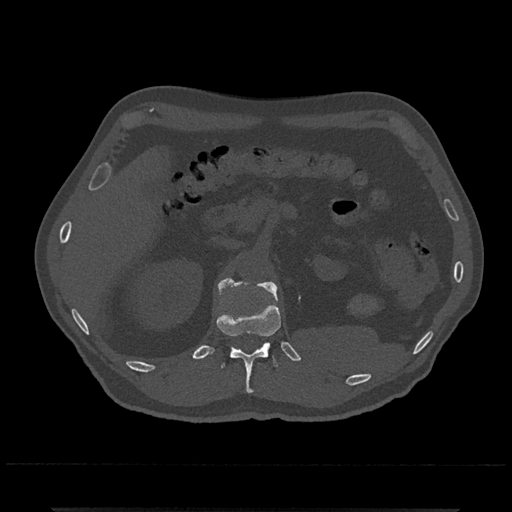
CT including the spine, one axial slice; slice 414 of 797 in the series (ordered by position); reconstruction kernel Br40s/3; 120 kVp; bone window (W 1800 / L 400 HU); 512 × 512 image matrix, field of view 393 × 393 mm. Patient: male, 67 years. Case-level facts recorded for this patient, not image findings: primary cancer: prostate.
Structures marked on this image (semi-automatic segmentation, software-assisted and operator-edited):
- L1 vertebra: box from (x=218, y=278) to (x=278, y=301) px
- T12 vertebra: (x=217, y=291)–(x=281, y=394)